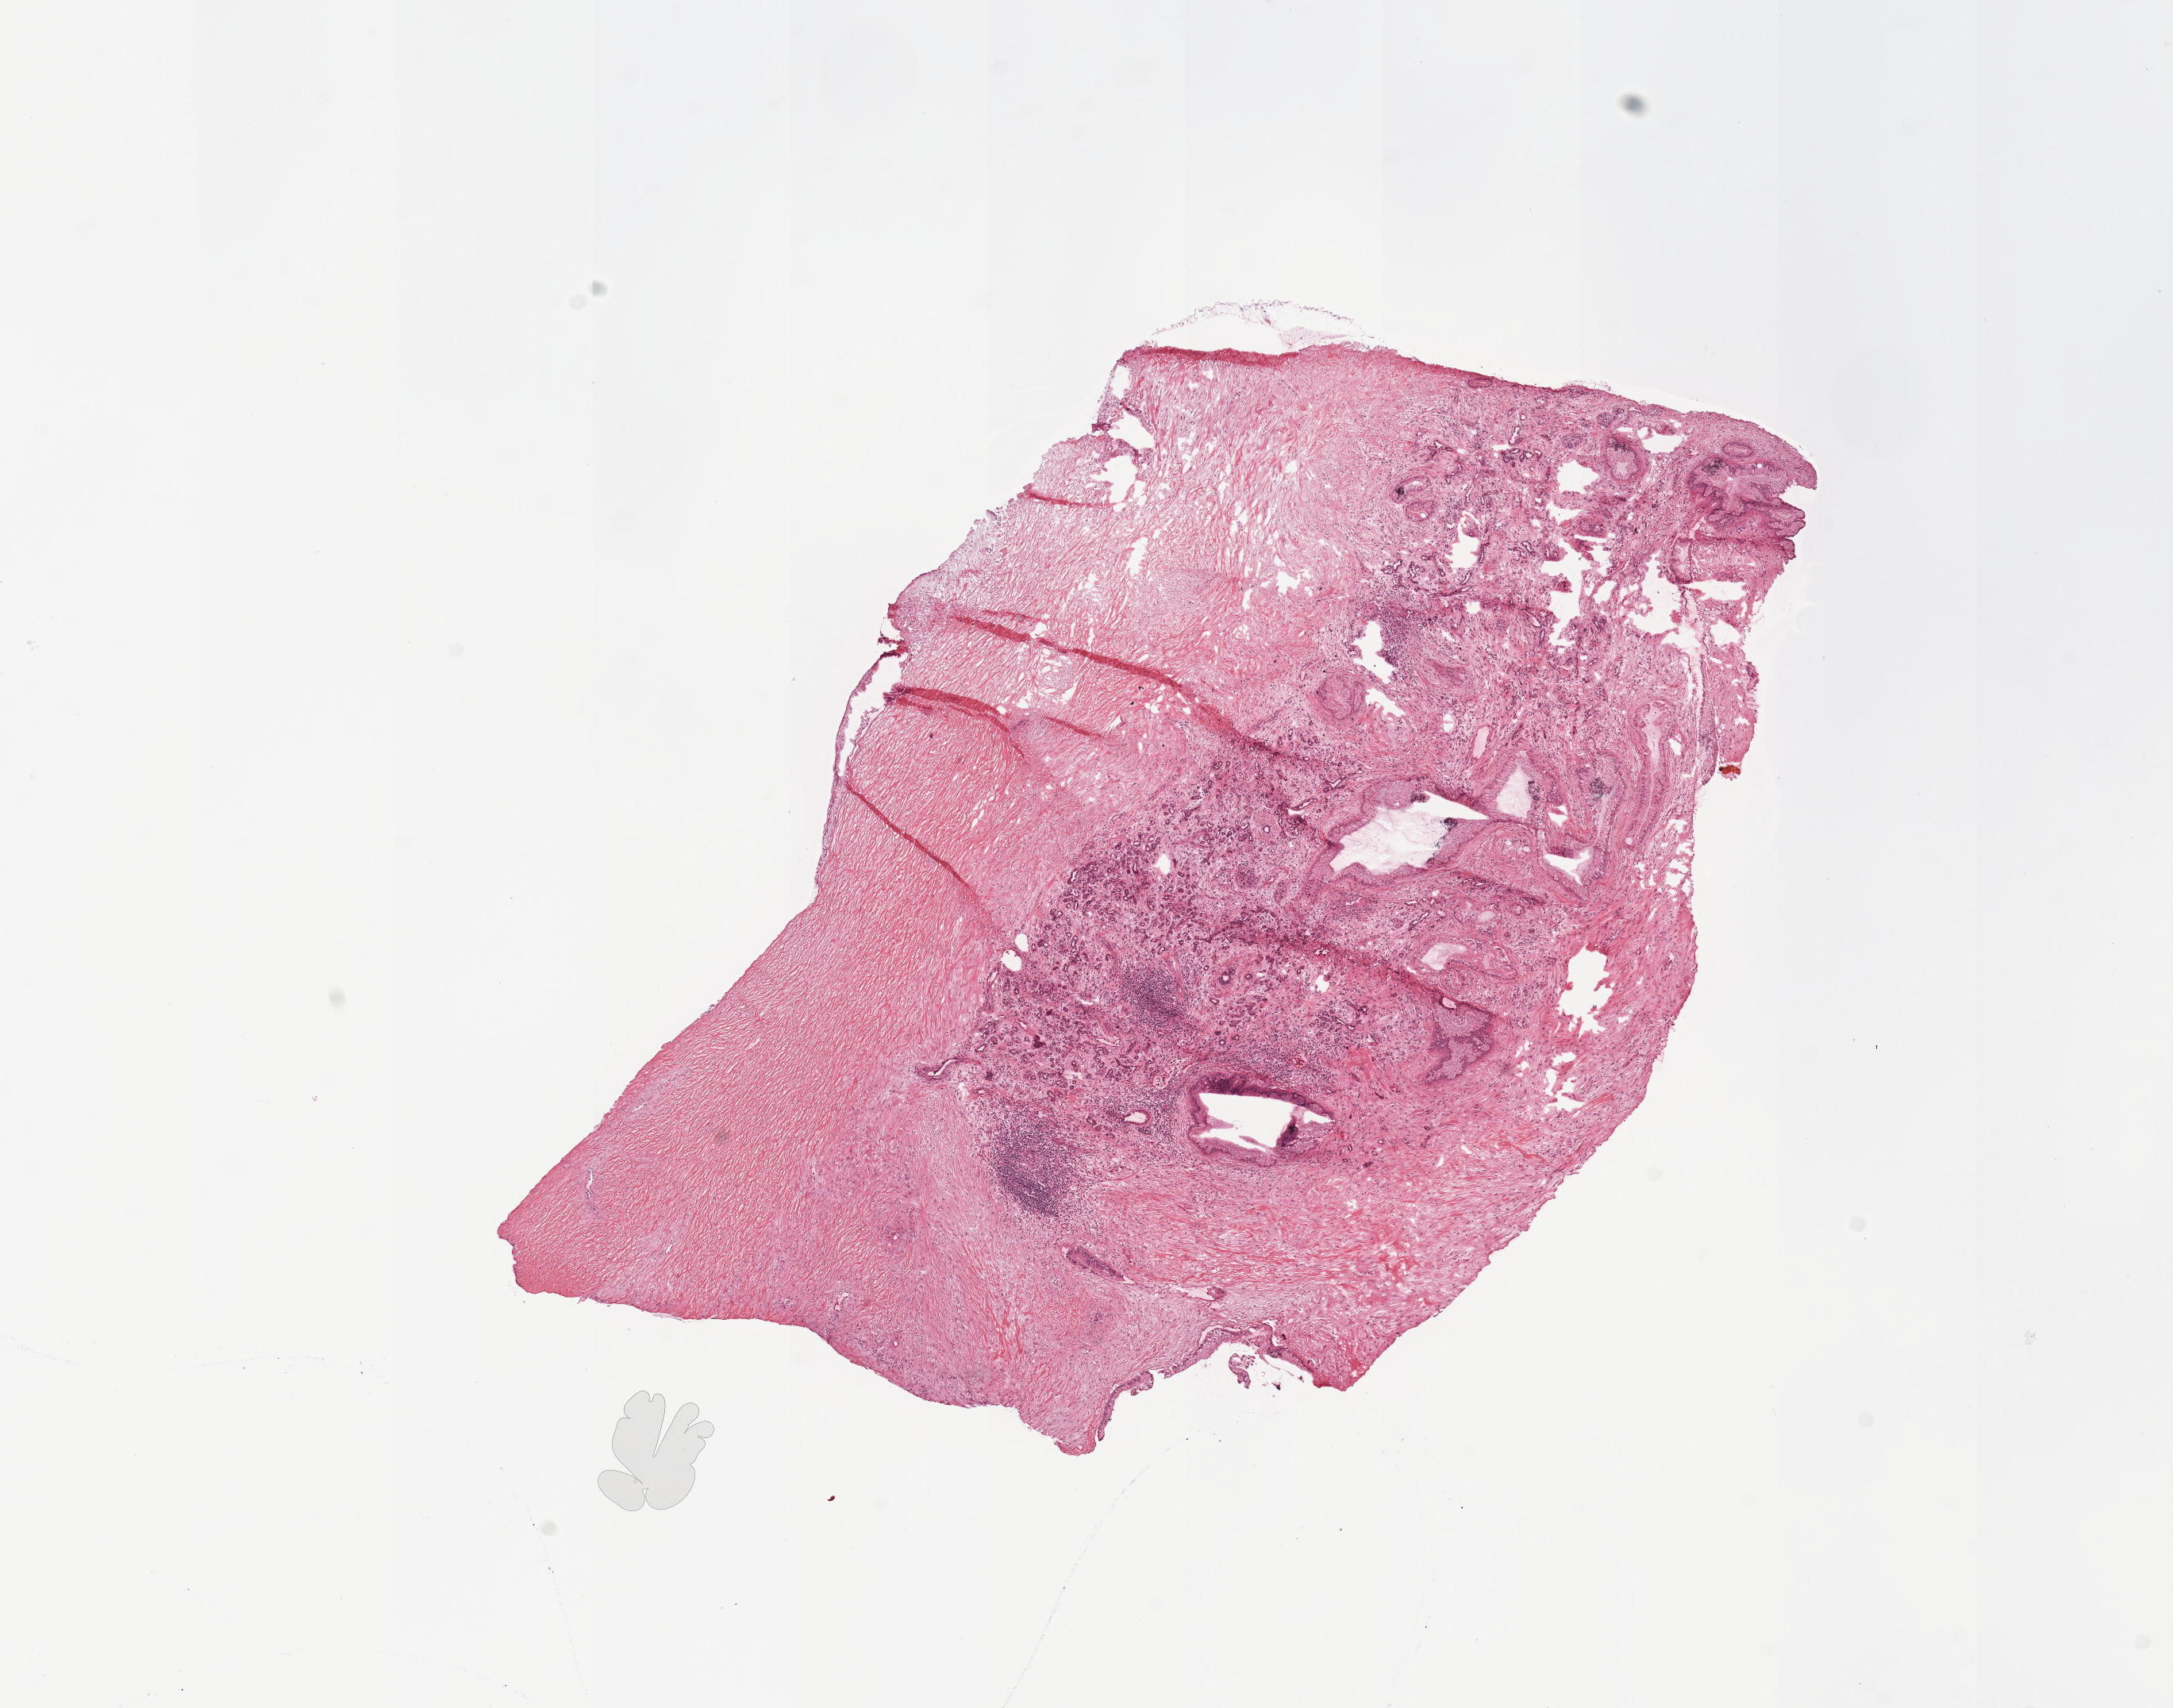
Digitized Hematoxylin and eosin (H&E) stained tissue section (whole slide), low-resolution overview of the scanned area, about 10.8 x 8.5 mm (from a 20x scan); pancreas, tumour tissue. 75-year-old male patient.
Patient diagnosis (cohort enrolment): ductal adenocarcinoma (pancreas).